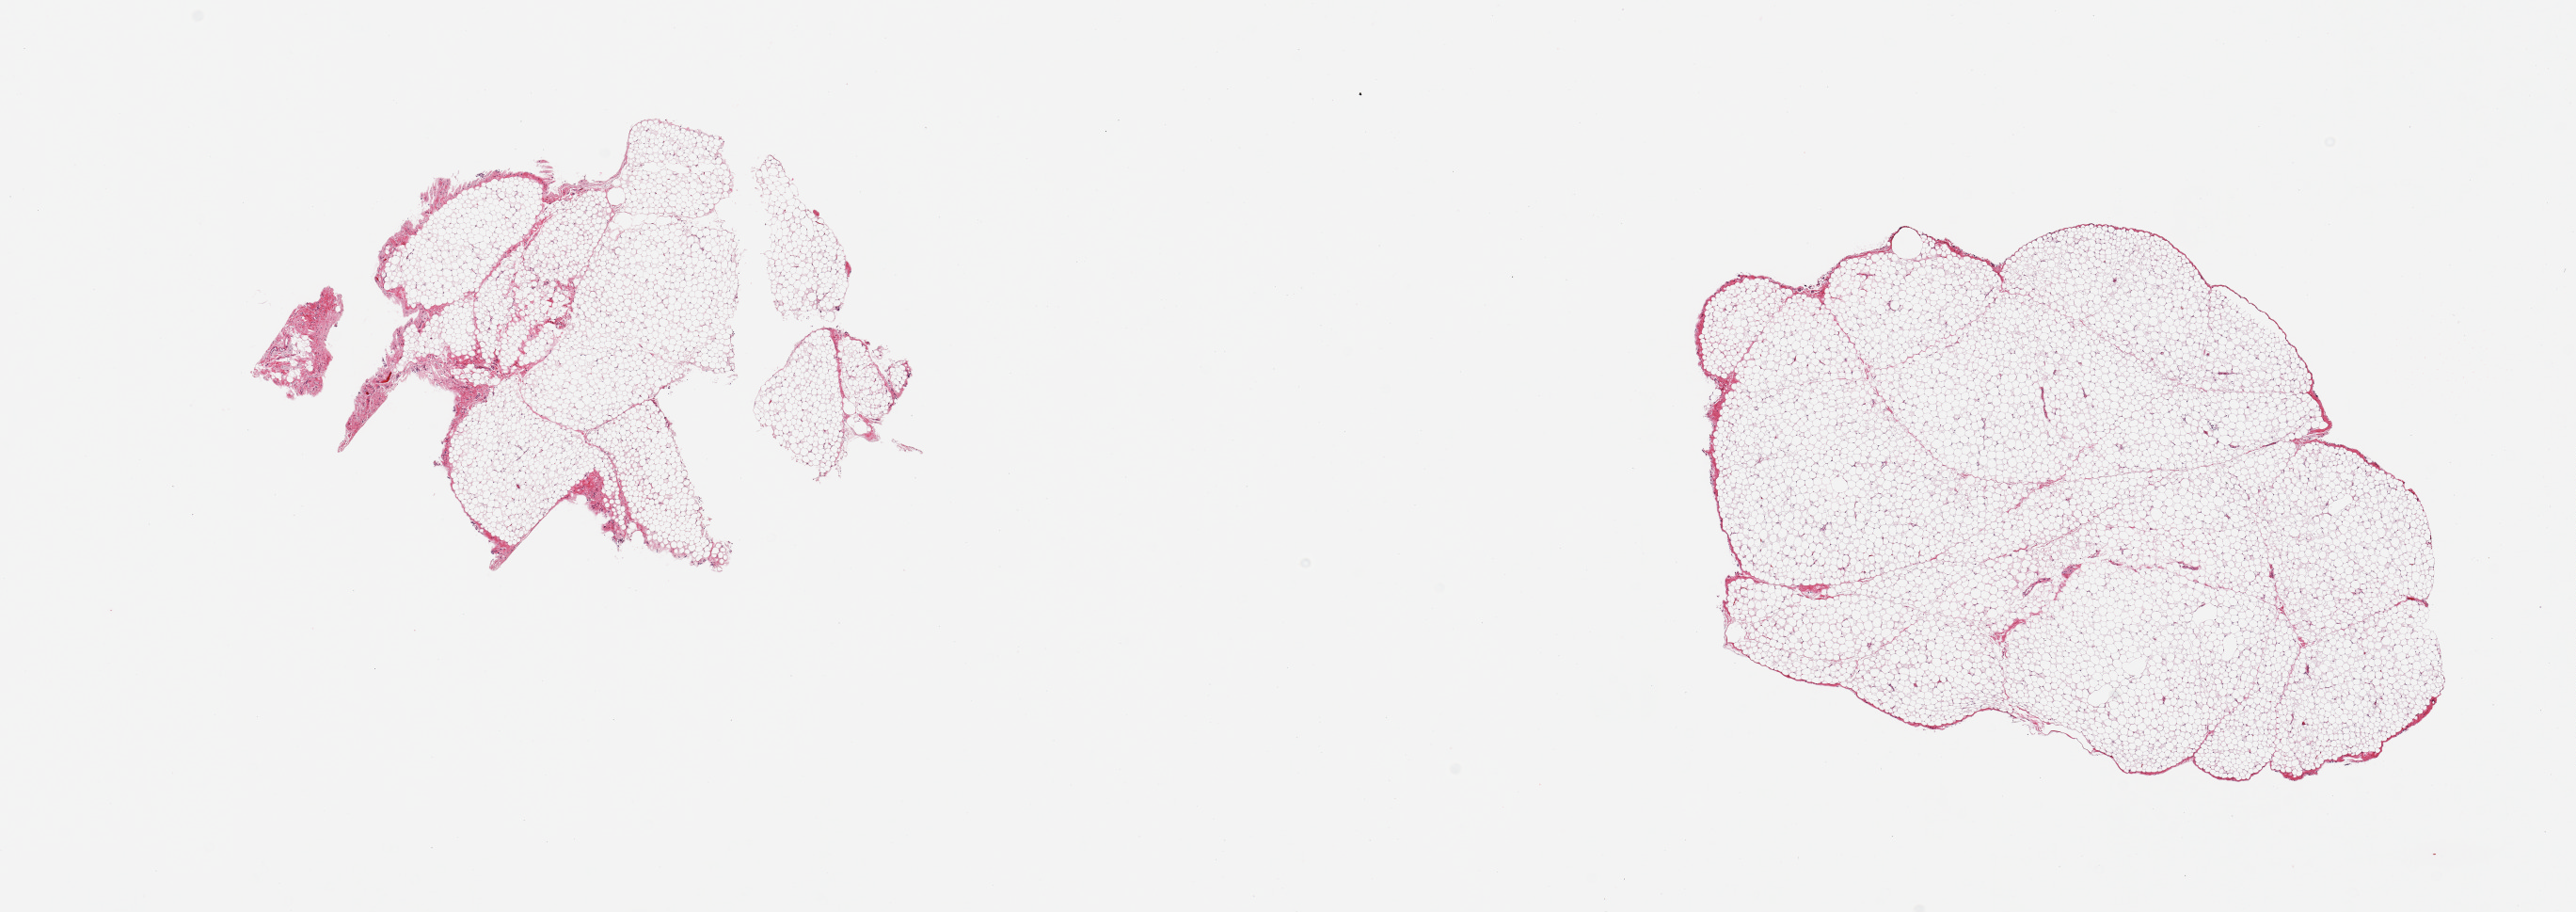
Whole-slide image, H&E stain, brightfield, low-resolution overview of the scanned area, about 21.7 x 7.7 mm (from a 20x scan). PAXgene-fixed paraffin-embedded (PFPE) section. Section of omentum (target tissue). Tissue donor sample. Donor: female.
Reviewer comment on this tissue sample: 2 pieces; mature adipose tissue.